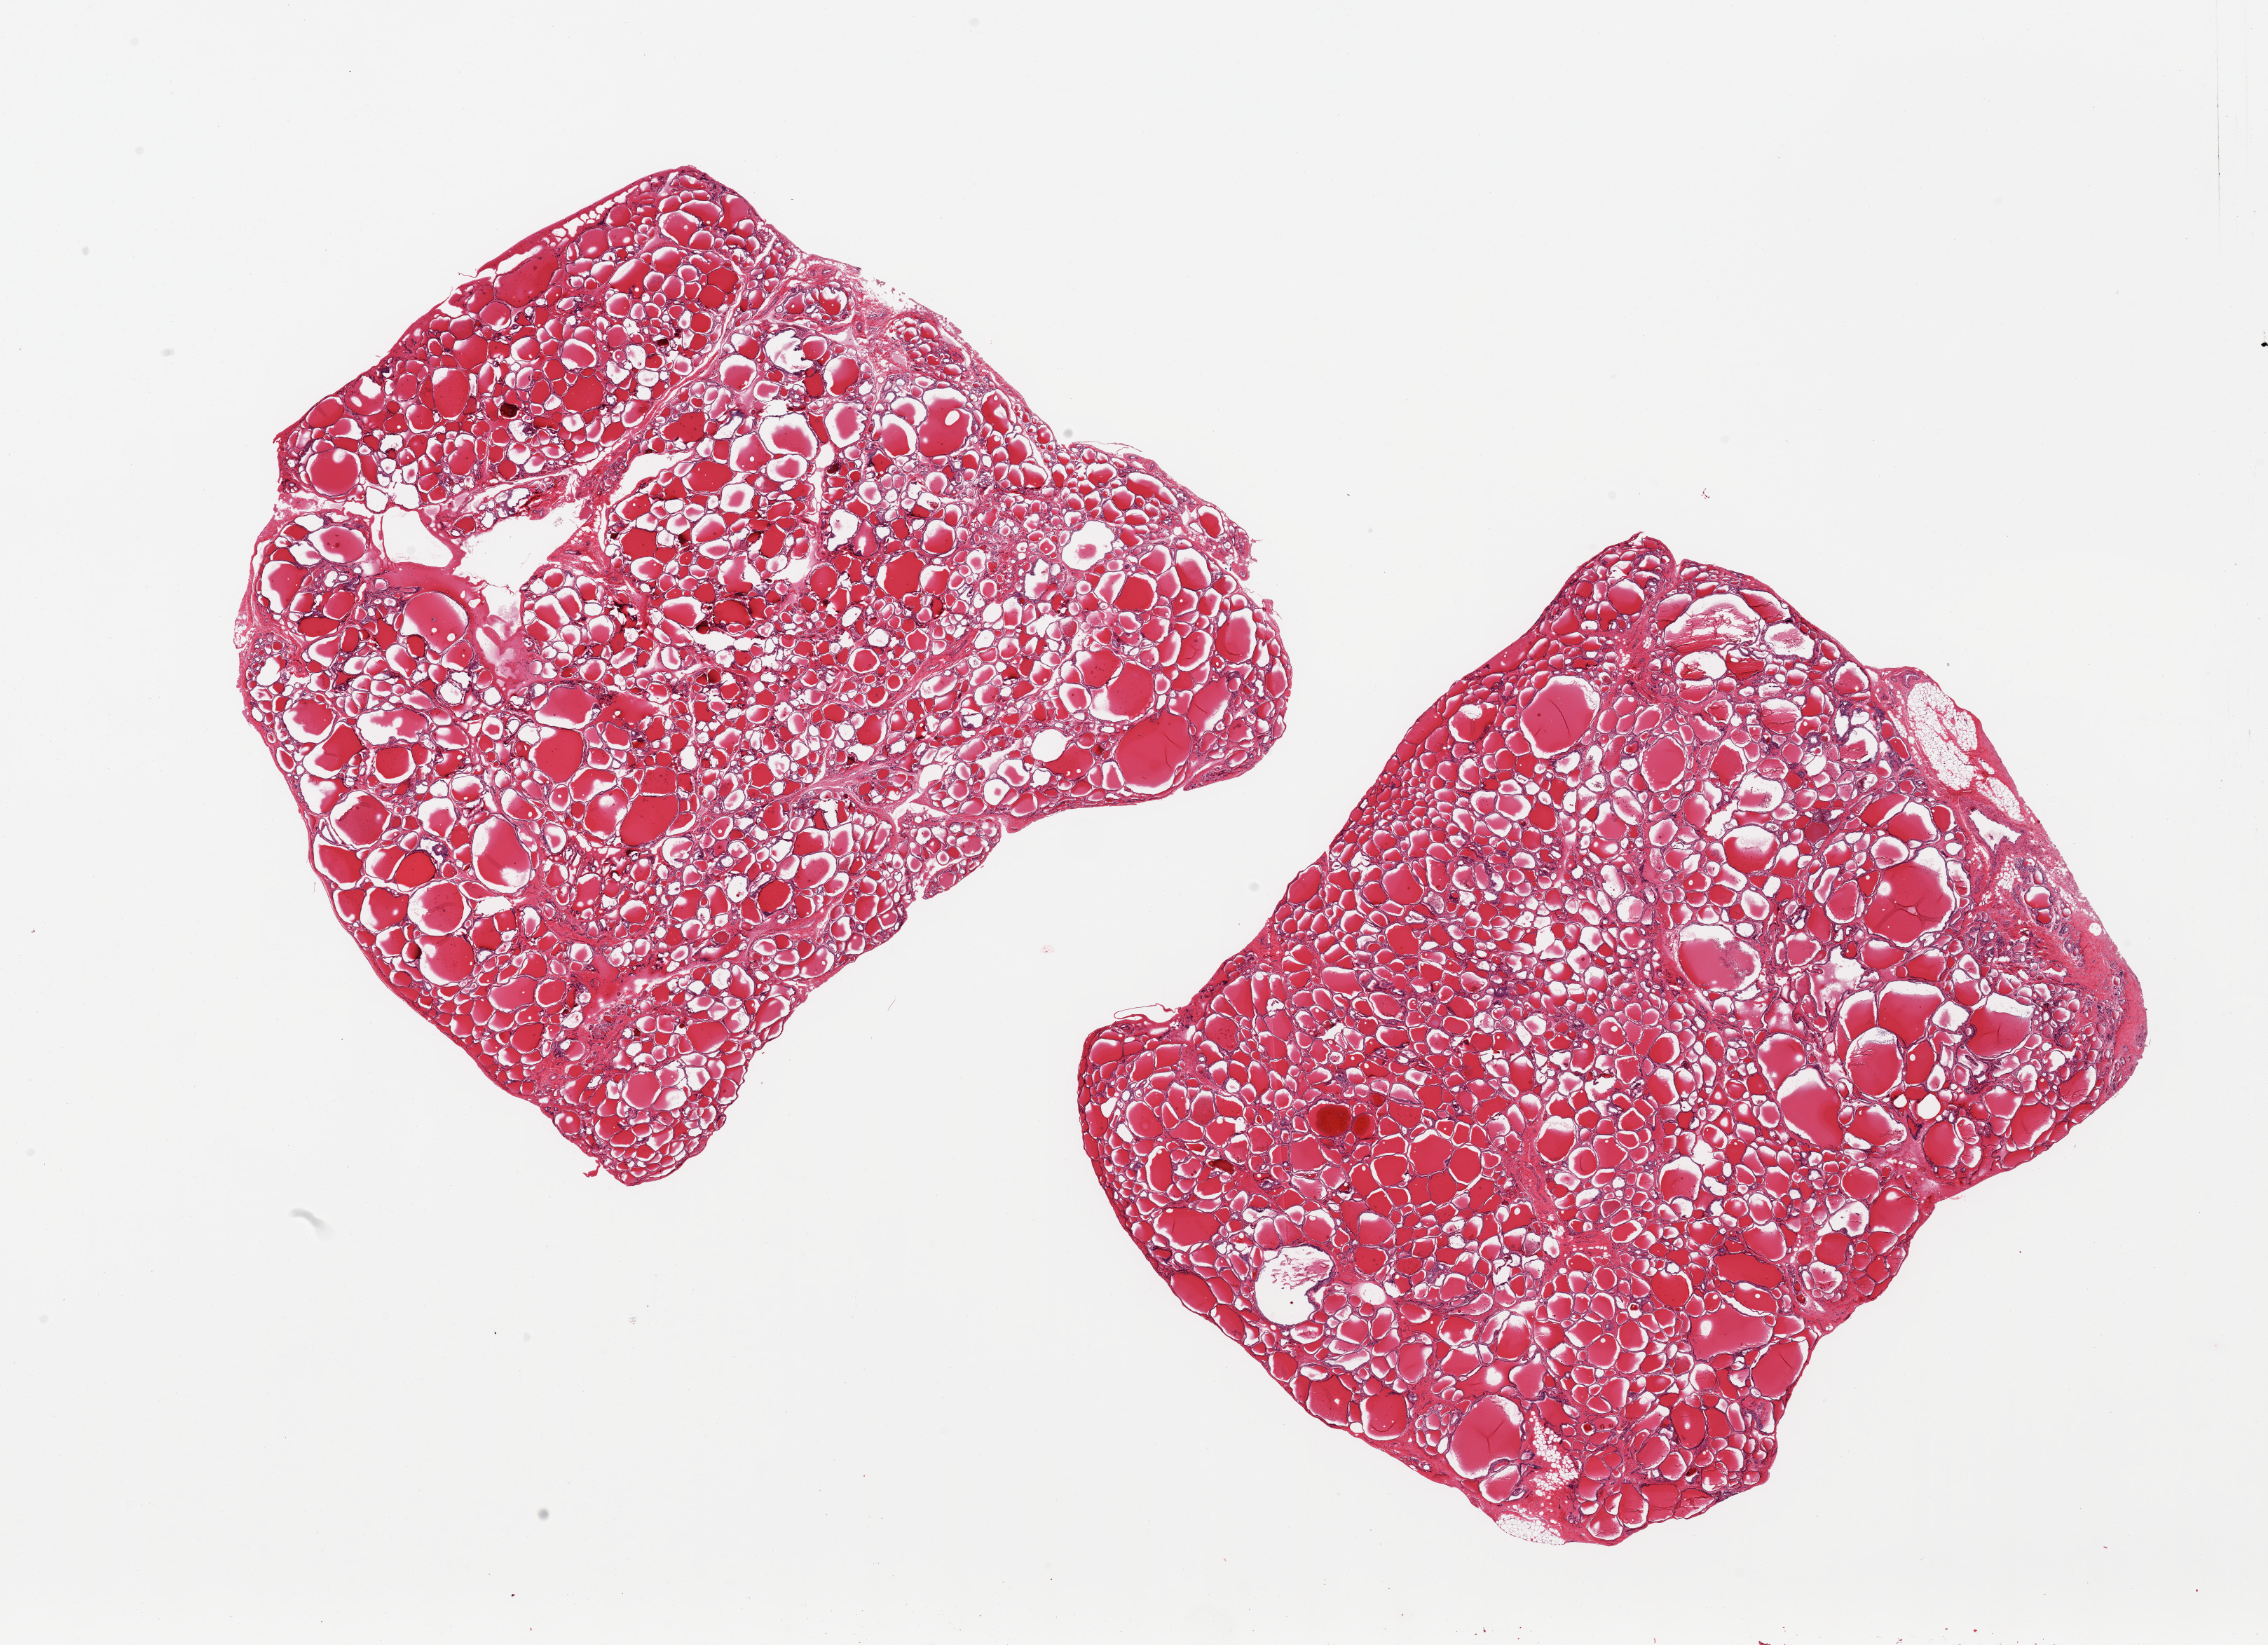
Whole-slide image, hematoxylin and eosin (H&E) stain, brightfield, low-resolution overview of the scanned area, about 25.6 x 18.6 mm (slide scanned at 20x). PAXgene-fixed paraffin-embedded (PFPE) section. Sampled site (target tissue): thyroid. Tissue donor sample. Donor sex: male.
Reviewer comment on this tissue sample: 2 pieces; 1 includes minimal portion of fat.